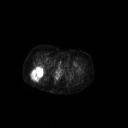
FDG PET of an extremity soft-tissue mass (from a PET/CT study), one axial slice. Position 54 of 267 along the scan axis. 128 × 128 image matrix. Patient: female, 70 years. Case-level facts recorded for this patient, not image findings: histological type: synovial sarcoma; grade: intermediate; site of the primary tumour: right buttock.
Structures marked on this image (expert contour drawn on MRI and transferred to this co-registered scan by the dataset authors):
- gross tumour volume including surrounding oedema: bounding box [x1, y1, x2, y2] px = [31, 65, 44, 82]
- gross tumour volume (mass): [31, 65, 44, 81]